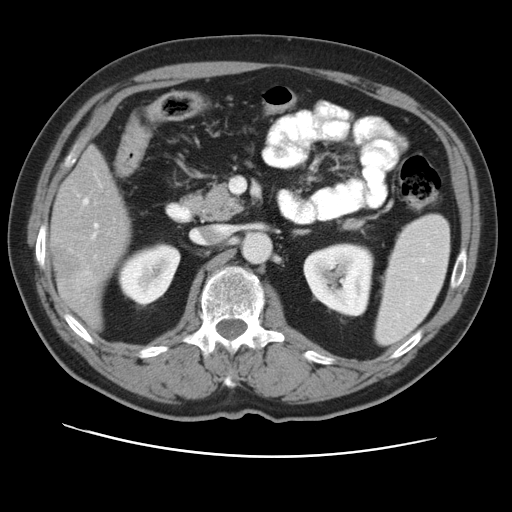
Contrast-enhanced abdominal CT, one axial slice. Position 21 of 49 along the scan axis. Intravenous contrast given. Soft-tissue window (W 400 / L 40 HU). 512 × 512 image matrix. Male patient, age 59 years. From the clinical record (not read from this slice): diagnosis: colorectal cancer liver metastases, imaged before liver resection; multiple liver metastases: yes; largest metastasis: 6.3 cm.
Annotated regions visible in this slice (outlined manually by an expert reader):
- hepatic veins: bounding box <84,199,88,204> (left, top, right, bottom; pixels)
- liver: <53,150,129,322>
- planned liver remnant (the part of the liver to remain after resection): <57,150,129,245>
- portal vein (with intrahepatic branches): <92,224,98,238>
- liver metastasis: <54,245,82,292>